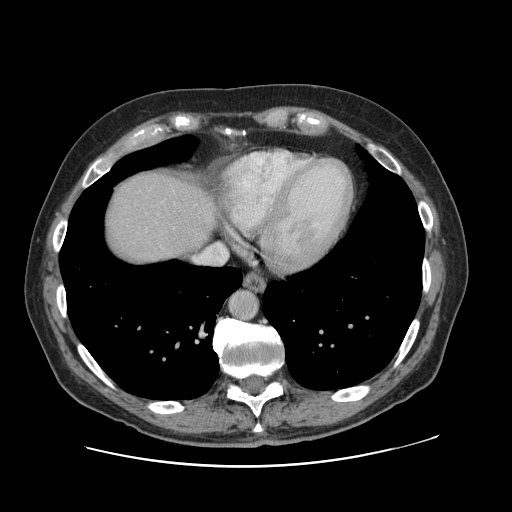
Contrast-enhanced abdominal CT, one axial slice. Slice 111 of 138 in the series (ordered by position). Intravenous contrast given. Soft-tissue window (W 400 / L 40 HU). 2.5 mm slice thickness. 512 × 512 image matrix, field of view 402 × 402 mm. Male patient, age 71 years. Case-level facts recorded for this patient, not image findings: diagnosis: colorectal cancer liver metastases, imaged before liver resection; multiple liver metastases: no; largest metastasis: 3.3 cm; disease in both lobes: no.
Structures marked on this image (manually delineated by an expert):
- hepatic veins: bounding box <197,243,228,266> (left, top, right, bottom; pixels)
- liver: <104,169,217,266>
- planned liver remnant (the part of the liver to remain after resection): <104,171,212,266>